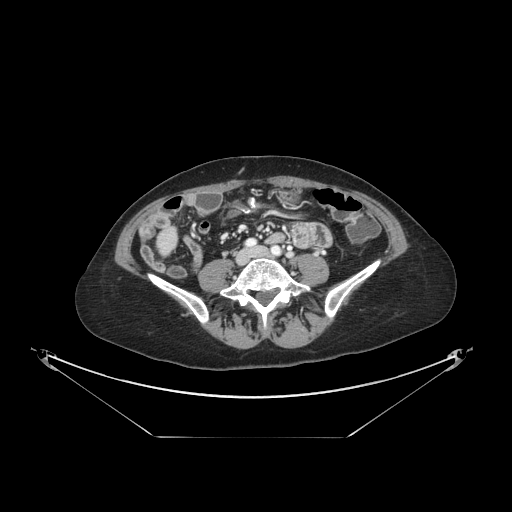
Contrast-enhanced abdominal CT, one axial slice; position 16 of 148 along the scan axis; reconstruction kernel STANDARD; 120 kVp; intravenous contrast given; soft-tissue window (W 400 / L 40 HU); 2.5 mm slice thickness; 512 × 512 image matrix, field of view 500 × 500 mm. Female patient, age 73 years. From the clinical record (not read from this slice): diagnosis: colorectal cancer liver metastases, imaged before liver resection; multiple liver metastases: no; largest metastasis: 1 cm; disease in both lobes: no.
Annotated regions visible in this slice (outlined manually by an expert reader):
- liver: bounding box (x1, y1, x2, y2) in pixels: (158, 232, 175, 252)